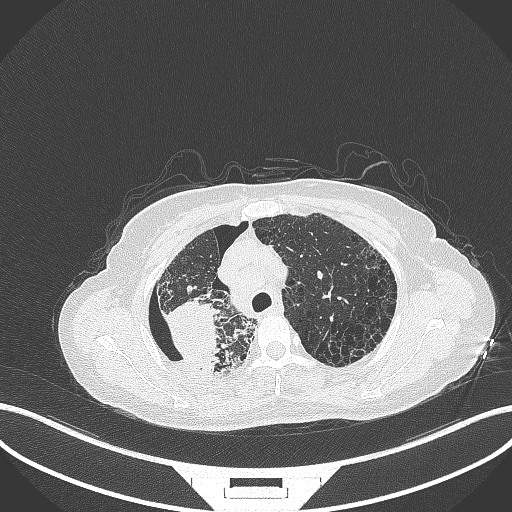
Chest CT, one axial slice. Position 272 of 408 along the scan axis. Reconstruction kernel B70f. 120 kVp. Lung window (W 1500 / L -600 HU). 512 × 512 image matrix, field of view 400 × 400 mm. Female patient, age 64 years. From the clinical record (not read from this slice): clinical TNM (as recorded): T3 N3 M0.
Structures marked on this image (rectangle marked by the reading radiologist):
- lung tumour (recorded histology: squamous cell carcinoma): bounding box [x1, y1, x2, y2] px = [161, 296, 223, 371]